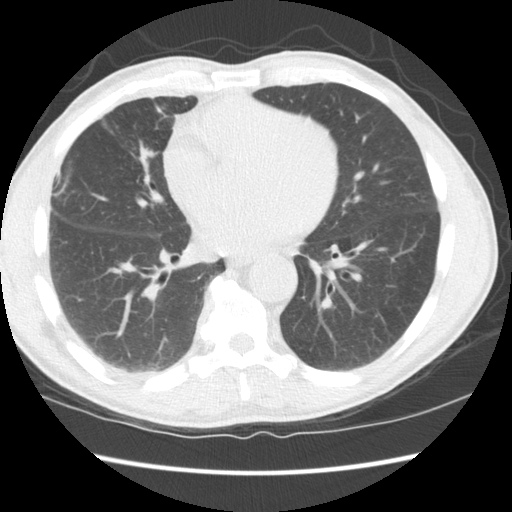
Chest CT (low-dose screening protocol), one axial image; third annual screen; lung window (W 1500 / L -600 HU); 2.5 mm slice thickness. Male, age 65 years at enrolment. Current smoker at enrolment.
Lesion marked by an expert reader, box from (x=108, y=134) to (x=169, y=207) px. Reader record for this screening exam (exam-level; its link to the box is not recorded): non-calcified nodule or mass ≥4 mm, right middle lobe, 16 × 15 mm, smooth margins, soft tissue attenuation, pre-existing on the prior screen: yes; interval growth: yes. Official screen result: positive, other. Later outcome: lung cancer diagnosed 357 days after this screen — squamous cell carcinoma, NOS, right middle lobe, poorly differentiated (G3), stage IA (AJCC 6th edition), 23 mm at pathology.